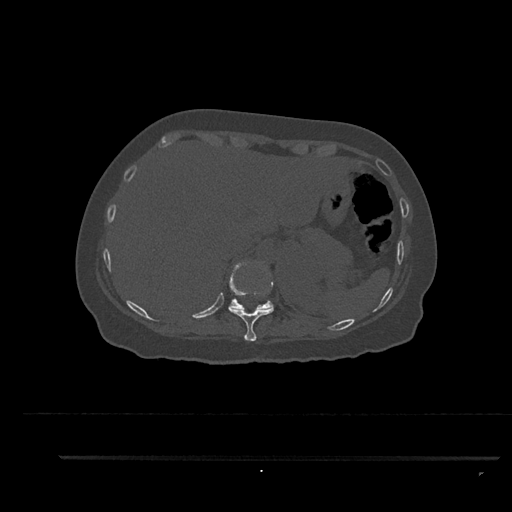
CT including the spine, one axial slice; position 344 of 797 along the scan axis; bone window (W 1800 / L 400 HU); 512 × 512 image matrix, field of view 408 × 408 mm. Female patient, age 44 years. From the clinical record (not read from this slice): primary cancer: renal; vertebrae with lytic lesions (as recorded): L1.
Annotated regions visible in this slice (semi-automatically segmented with operator editing):
- T10 vertebra: bounding box [x1, y1, x2, y2] px = [228, 289, 274, 341]
- T11 vertebra: [229, 262, 274, 310]